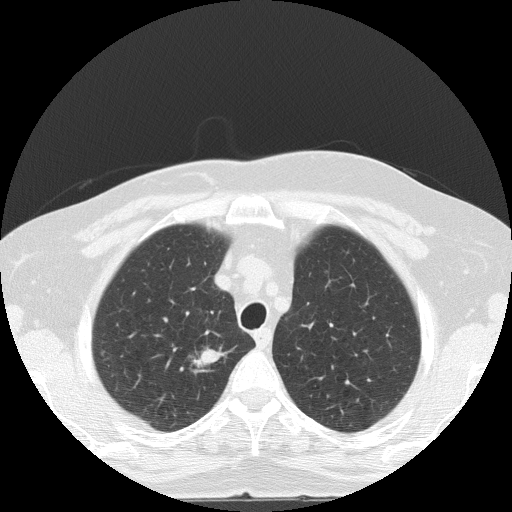
Low-dose screening chest CT, axial slice, baseline annual screen, lung window (W 1500 / L -600 HU), lung (sharp) reconstruction kernel (FC51), 120 kVp. Female participant, aged 56 years at enrolment.
• Lesion marked by an expert reader, bounding box [x1, y1, x2, y2] px = [169, 335, 236, 389].
• The screening reader recorded 2 non-calcified nodules or masses ≥4 mm on this exam (right upper lobe, right lower lobe); which of them this box marks is not recorded.
• Official screen result: positive, change unspecified: nodule(s) >= 4 mm or enlarging nodule(s), mass(es), or other non-specific abnormalities suspicious for lung cancer.